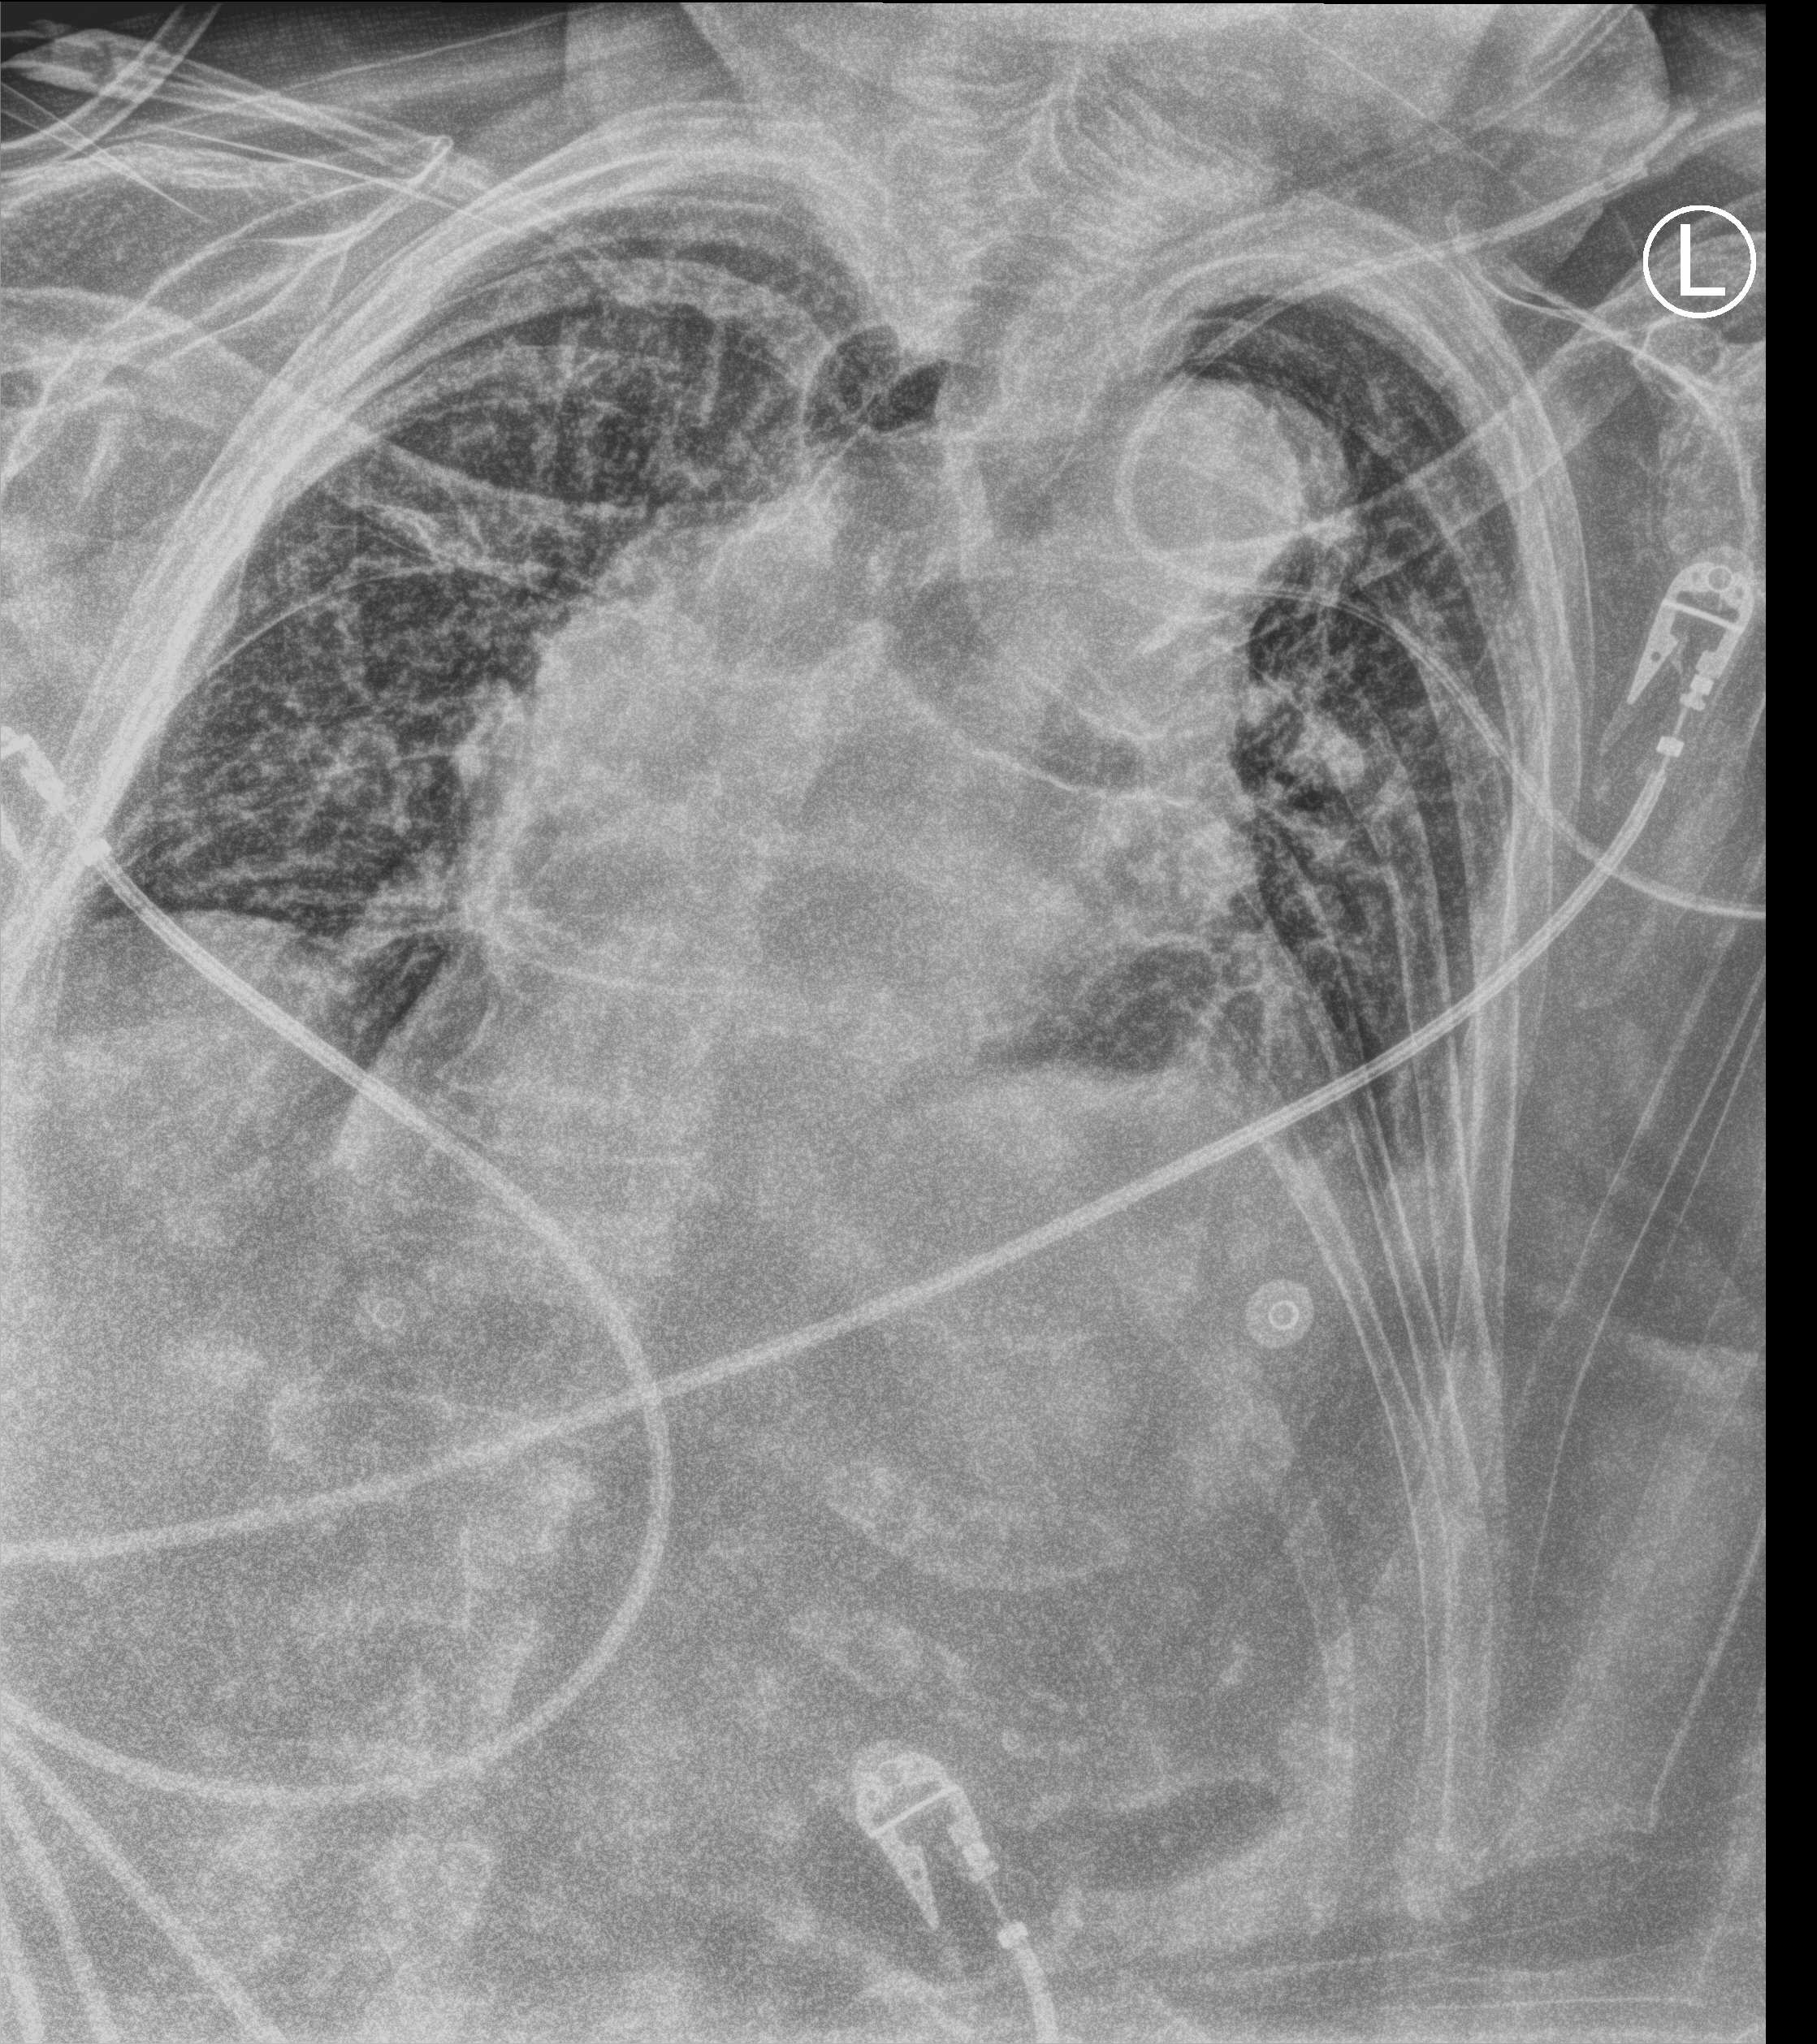
Portable chest radiograph; anteroposterior (AP) projection. Female patient hospitalised with COVID-19, age 75–90 years.
Hospital-stay facts (about this admission, not read from this image; timing relative to this image not recorded): admitted to intensive care during this hospital stay: yes; mechanically ventilated during this hospital stay: no.